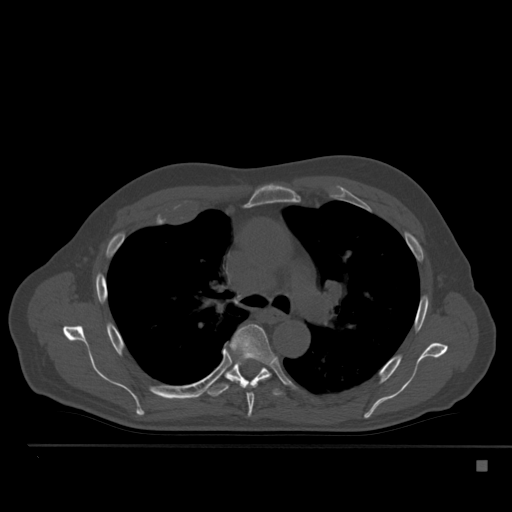
CT including the spine, one axial slice; slice 357 of 517 in the series (ordered by position); reconstruction kernel Br40s; bone window (W 1800 / L 400 HU); 1.5 mm slice thickness; 512 × 512 image matrix, field of view 408 × 408 mm. Patient: male, 70 years. Case-level facts recorded for this patient, not image findings: primary cancer: renal.
Structures marked on this image (semi-automatically segmented with operator editing):
- T5 vertebra: box from (x=229, y=324) to (x=275, y=417) px
- T6 vertebra: (x=205, y=359)–(x=286, y=397)